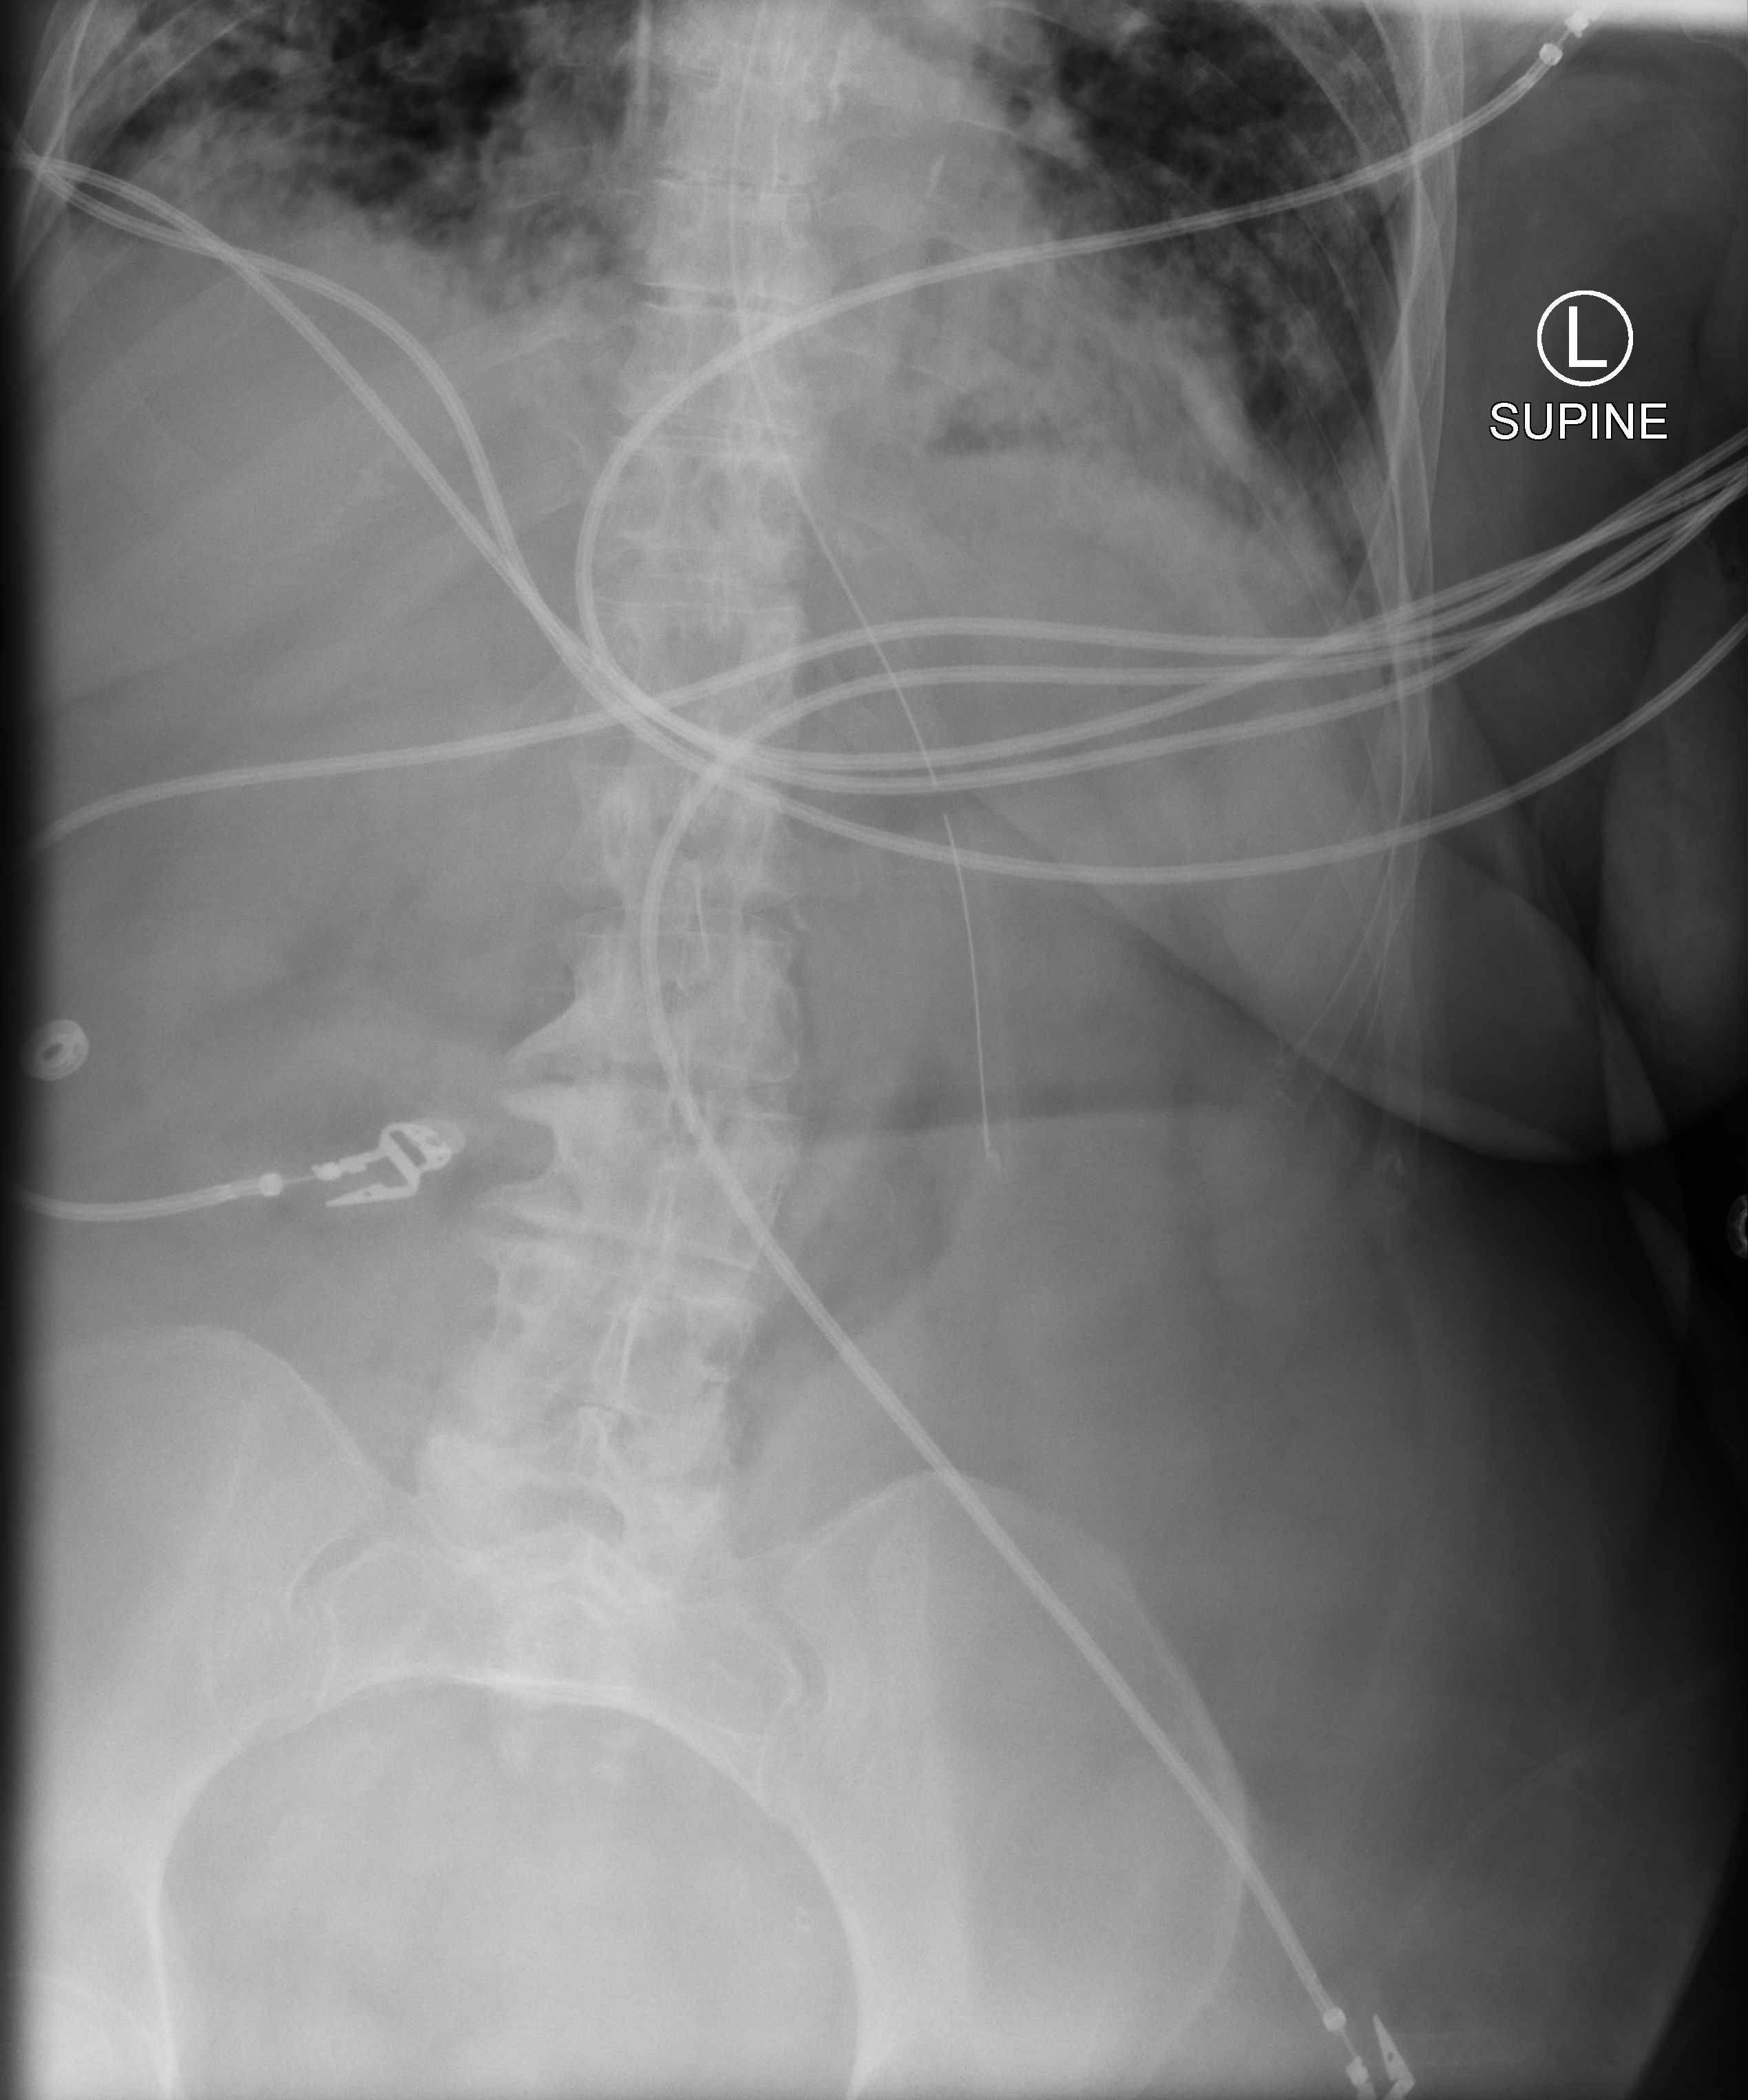
Bedside abdomen radiograph (computed radiography); anteroposterior (AP) projection. Female patient hospitalised with COVID-19, age 75–90 years.
From the hospital-stay record, not from the radiograph (when in the stay this image was taken is not recorded):
- COPD (admission record): no
- admitted to intensive care during this hospital stay: yes
- mechanically ventilated during this hospital stay: yes